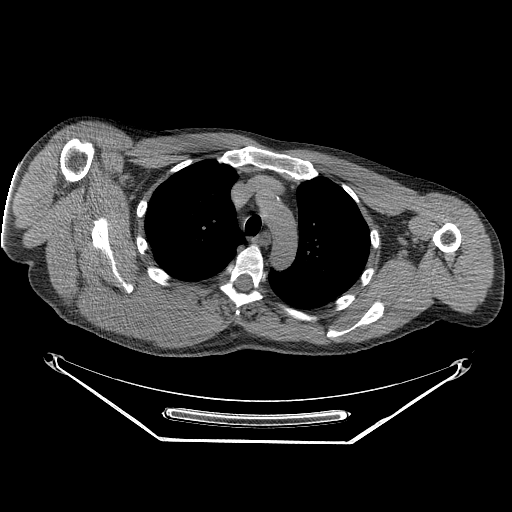
CT of an extremity soft-tissue mass (from a PET/CT study), one axial slice. Position 188 of 267 along the scan axis. 140 kVp. Soft-tissue window (W 400 / L 40 HU). 3.75 mm slice thickness. 512 × 512 image matrix, field of view 500 × 500 mm. Male patient. From the clinical record (not read from this slice): histological type: pleiomorphic spindle cell undifferentiated; grade: high; site of the primary tumour: right parascapusular.
Structures marked on this image (expert contour drawn on MRI and transferred to this co-registered scan by the dataset authors):
- gross tumour volume including surrounding oedema: box from (x=82, y=269) to (x=222, y=337) px
- gross tumour volume (mass): (x=82, y=270)–(x=202, y=334)